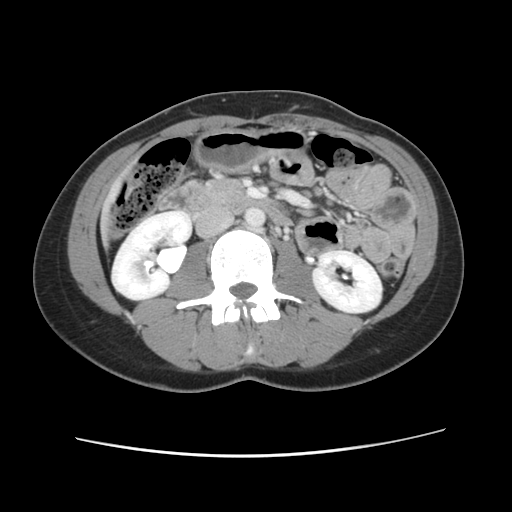
Contrast-enhanced abdominal CT, one axial slice; position 21 of 134 along the scan axis; intravenous contrast given; soft-tissue window (W 400 / L 40 HU); 2.5 mm slice thickness; 512 × 512 image matrix, field of view 339 × 339 mm. Female patient, age 33 years. From the clinical record (not read from this slice): diagnosis: colorectal cancer liver metastases, imaged before liver resection; multiple liver metastases: yes; largest metastasis: 4.5 cm.
Annotated regions visible in this slice (expert manual segmentation):
- liver: box from (x=102, y=172) to (x=128, y=240) px